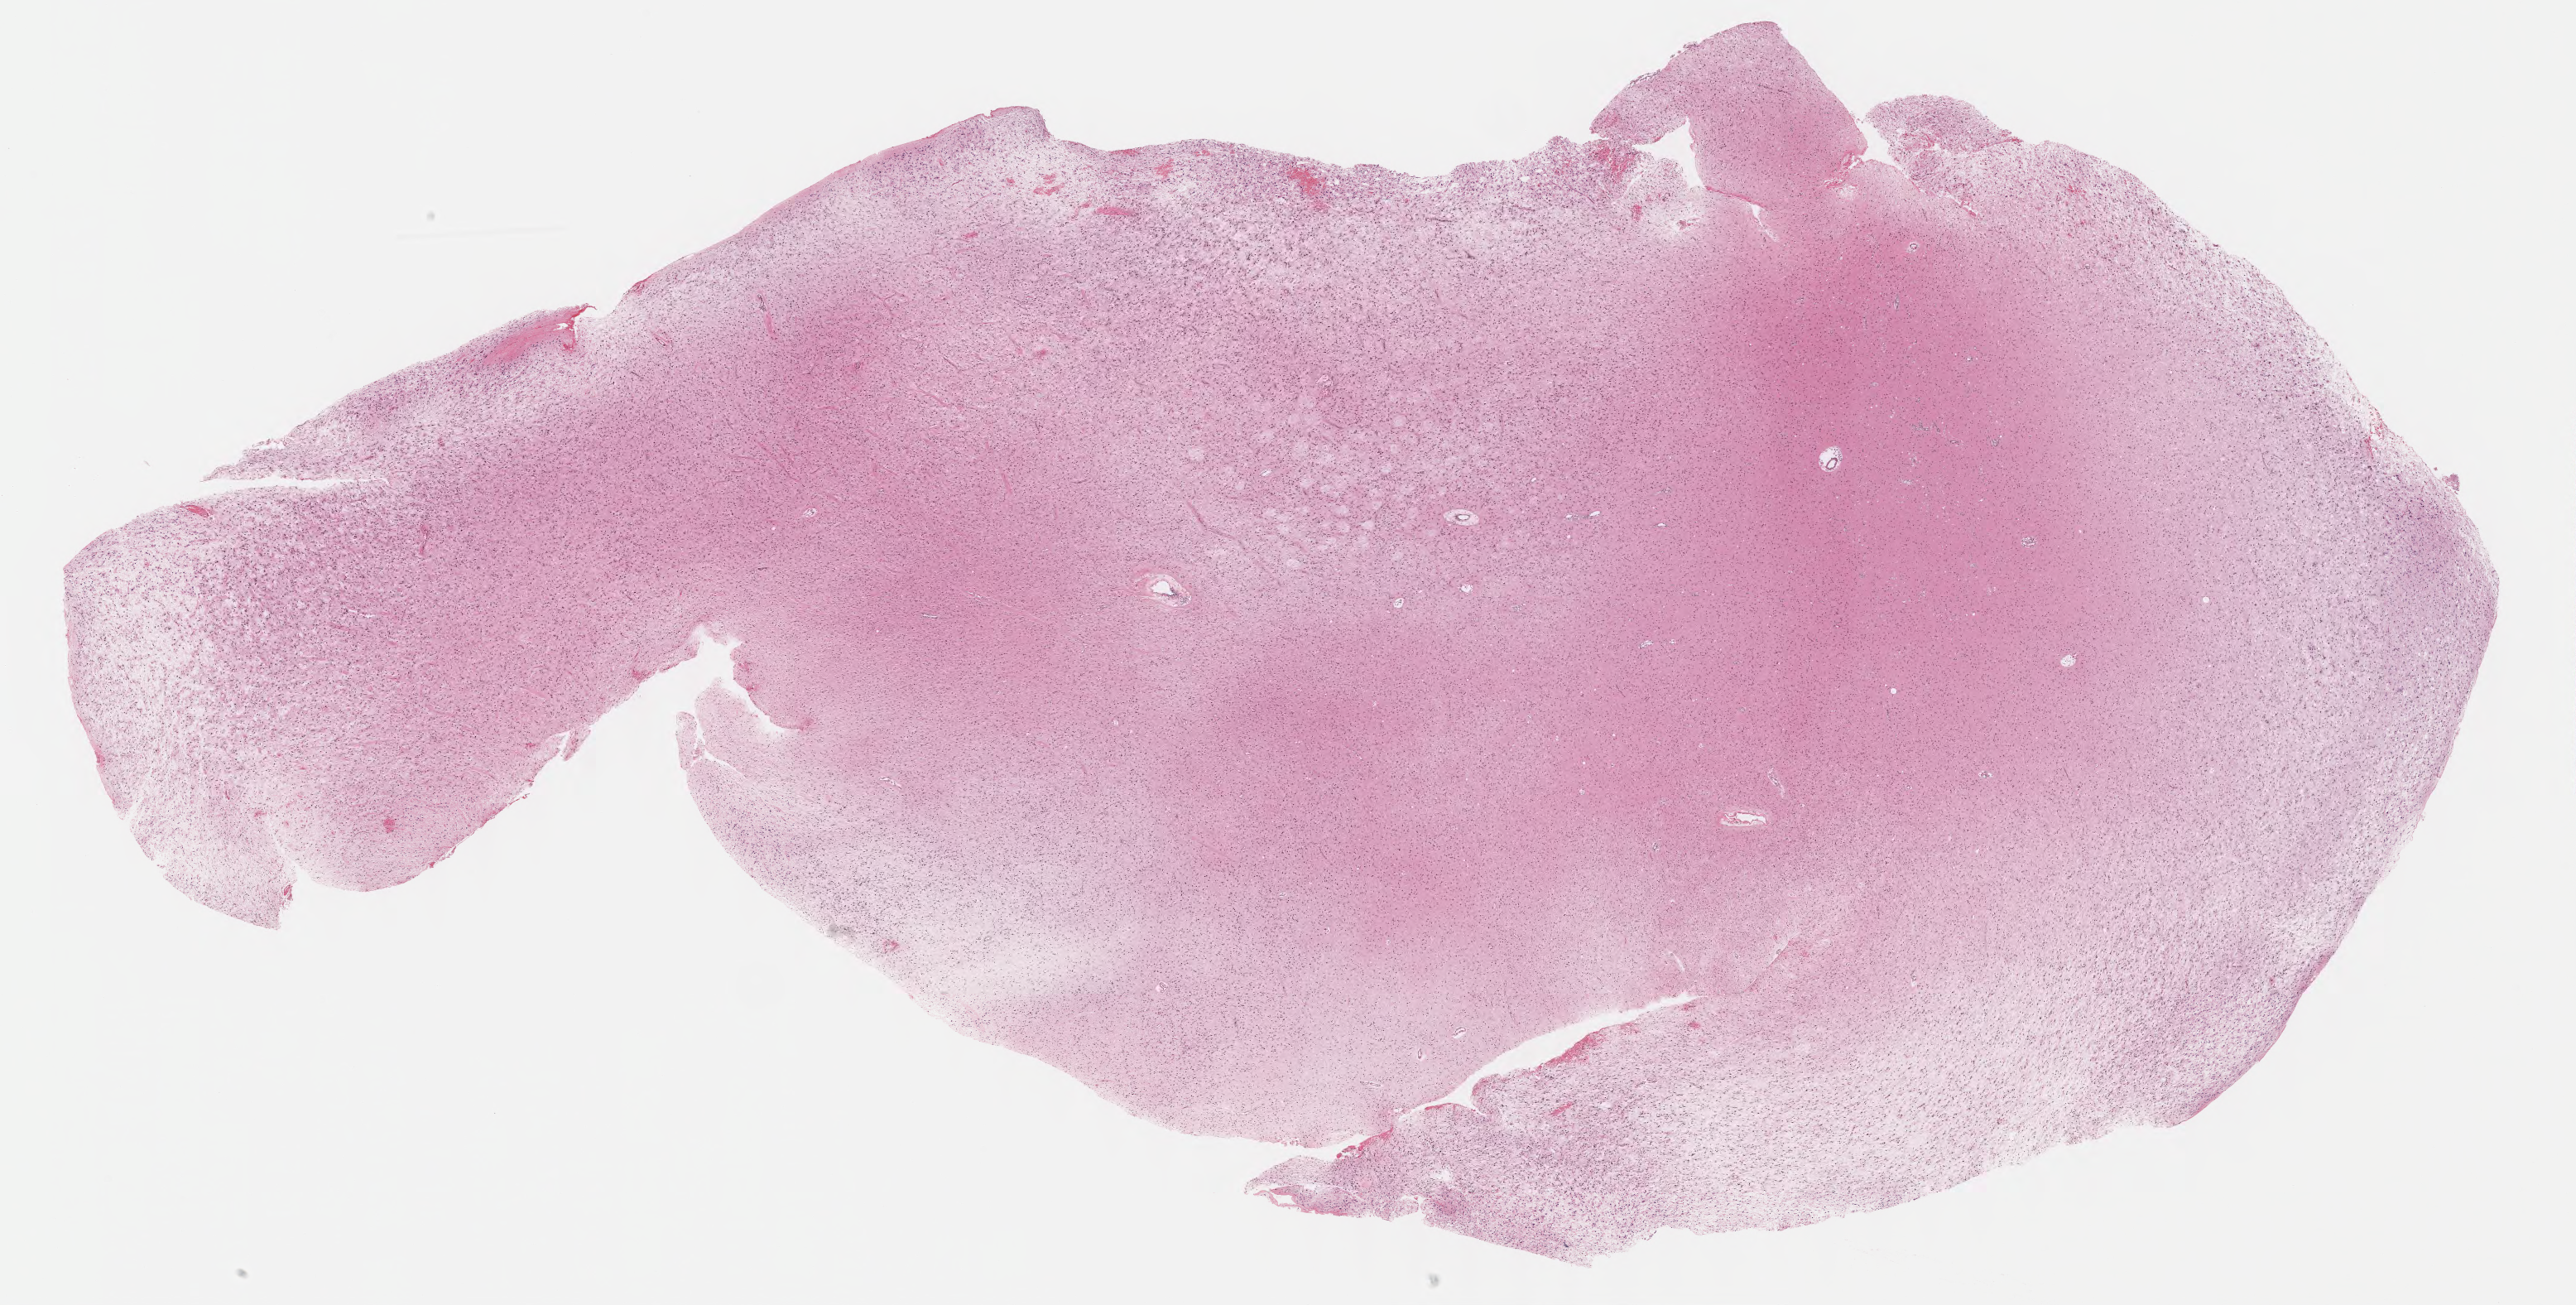
Hematoxylin and eosin (H&E) stained whole-slide image, low-resolution overview of the scanned area, about 24.6 x 12.5 mm, formalin-fixed paraffin-embedded (FFPE) diagnostic section, primary tumour sample from the brain. Patient: male, age at initial diagnosis 47 years.
Histologic diagnosis: Astrocytoma, NOS (cerebrum).